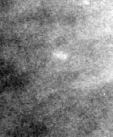
Region of interest cut from a scanned film mammogram (one marked finding), right breast, MLO view.
- Calcifications, morphology fine linear branching, distribution clustered / linear; BI-RADS assessment category 5; subtlety rating 4 on a 1 (subtle) to 5 (obvious) scale; pathology (as recorded): malignant.